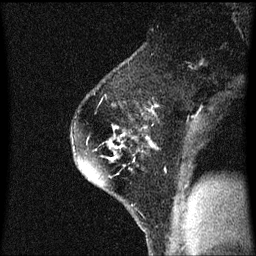
Breast MRI (dynamic contrast-enhanced), one sagittal slice. Position 43 of 60 along the scan axis. Dynamic contrast-enhanced series, image 2 of 3 at this slice position (ordered by acquisition). 1.5 T. TE 4.2 ms, TR 8.4 ms. 2 mm slice thickness. 256 × 256 image matrix, field of view 200 × 200 mm. Female patient, age 60 years.
Annotated regions visible in this slice (semi-automatically segmented with operator editing):
- analysis volume of interest (the breast-tissue region the enhancement analysis was run in; not a lesion): bounding box (x1, y1, x2, y2) in pixels: (70, 72, 135, 193)
- tumour enhancement mask (voxels above the 70 % enhancement threshold inside the analysis volume of interest): (94, 126, 125, 183)